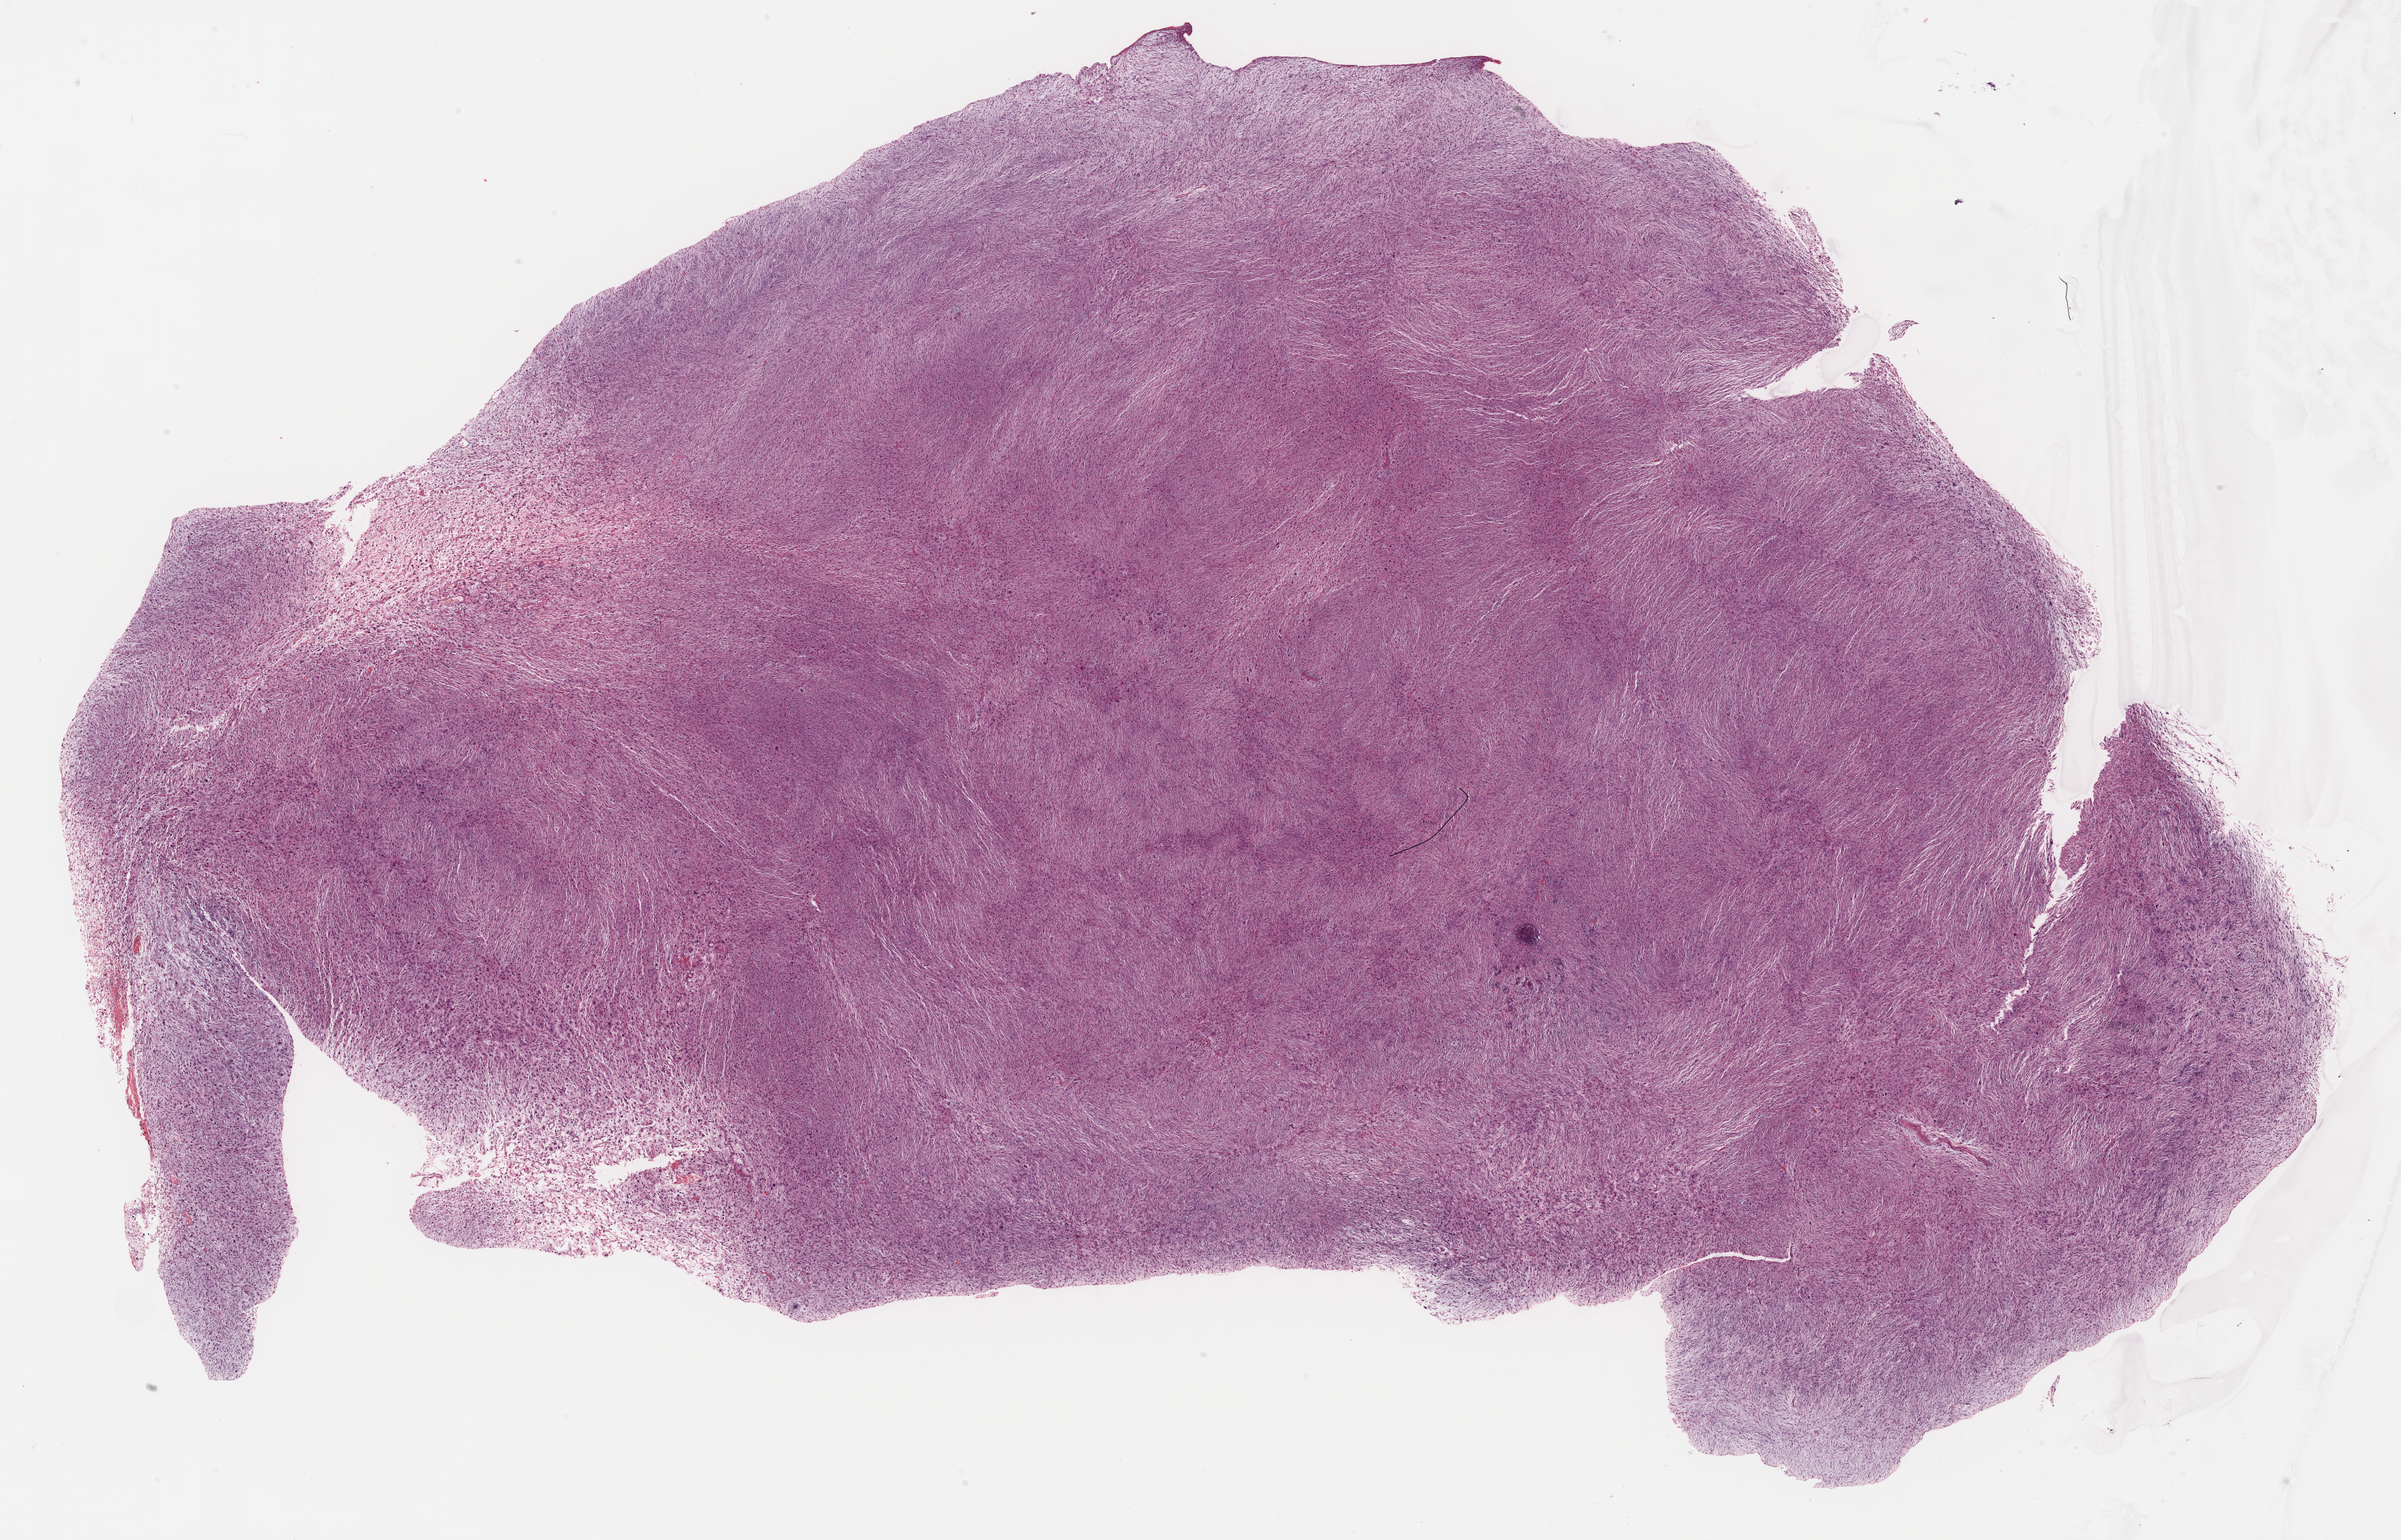
Whole-slide histology image, Hematoxylin and eosin (H&E) stained — whole scanned area (about 30.2 x 19.4 mm) shown as a low-resolution overview. Formalin-fixed paraffin-embedded (FFPE) diagnostic section. Connective, subcutaneous and other soft tissues, primary tumour sample. Patient sex: male.
• pathologic diagnosis: Fibromyxosarcoma (connective, subcutaneous and other soft tissues of trunk, NOS)